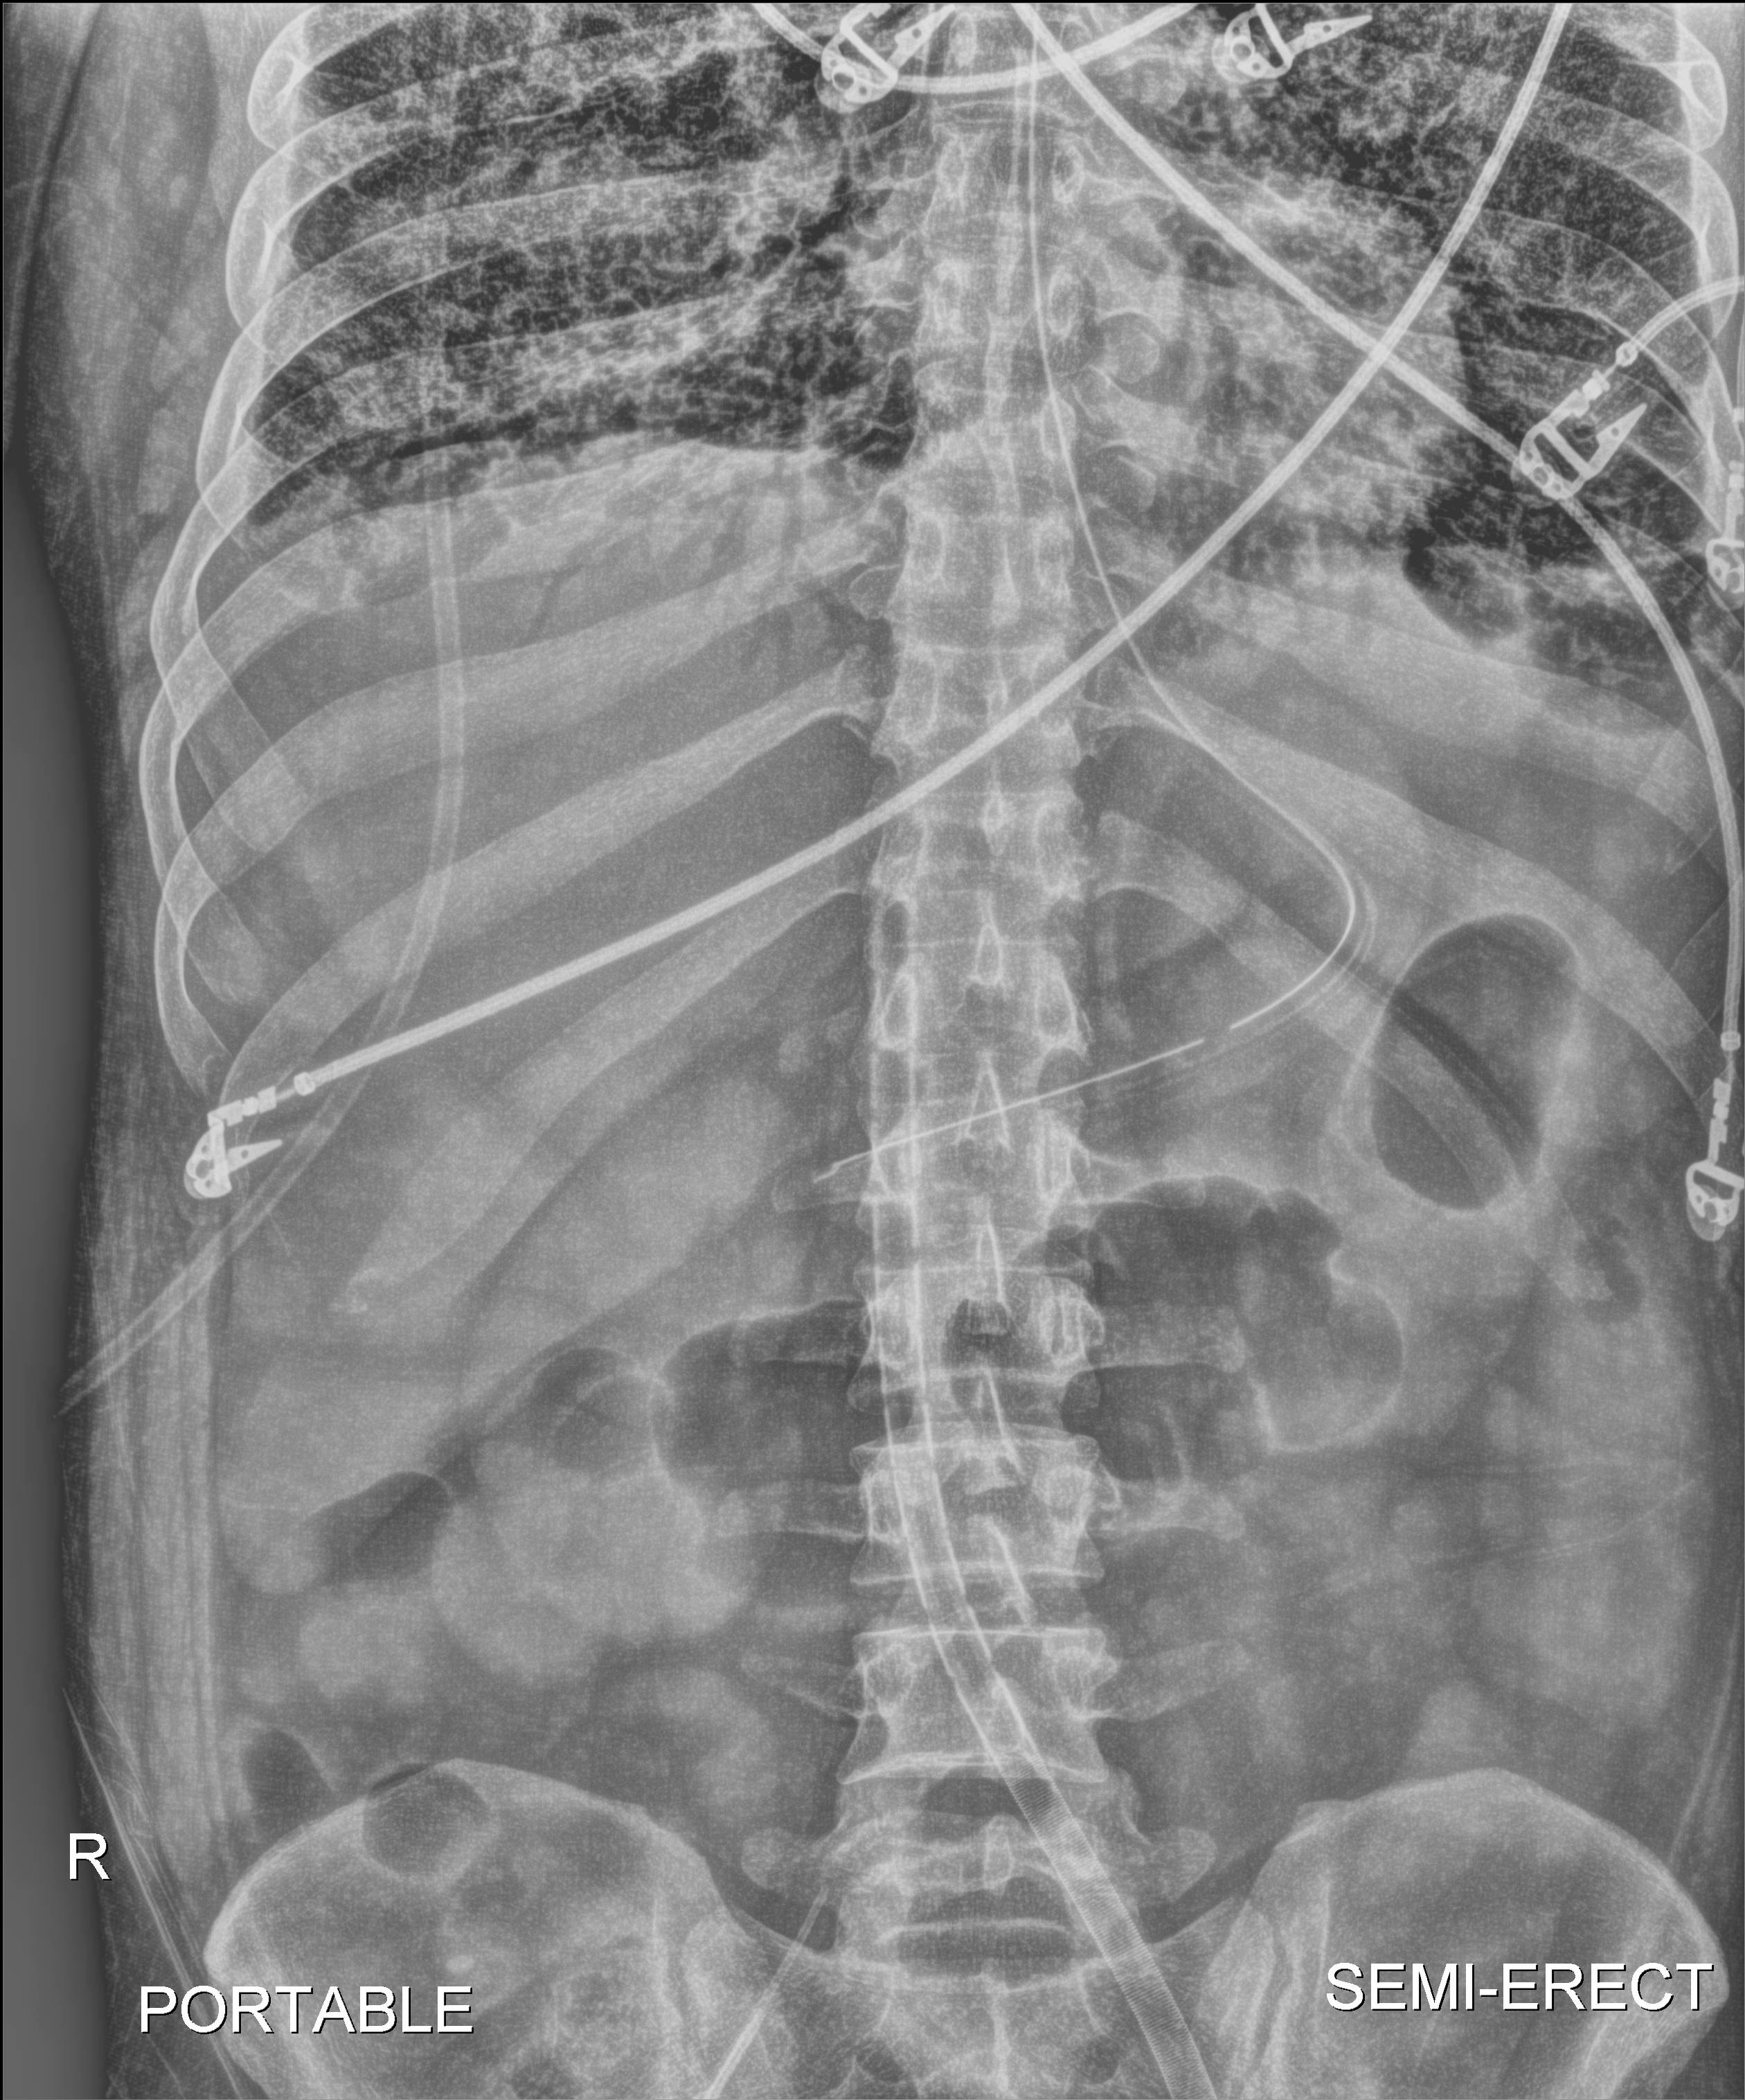
Bedside abdomen radiograph (digital radiography); anteroposterior (AP) projection. Patient hospitalised with COVID-19, aged 18–59 years.
Hospital-stay facts (about this admission, not read from this image; timing relative to this image not recorded): length of hospital stay: 60 days.